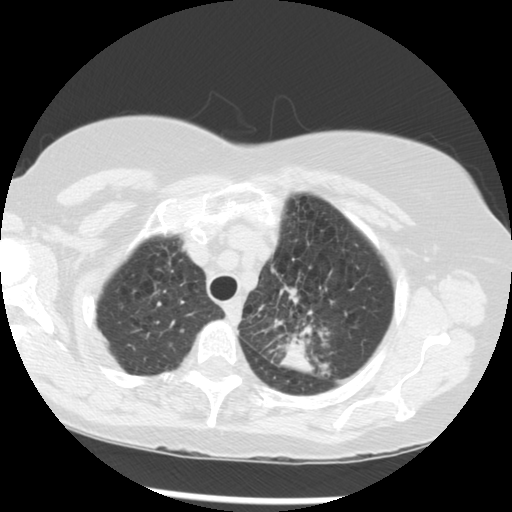
Chest CT (low-dose screening protocol), one axial image. Third screening round (two years after baseline). Lung window (W 1500 / L -600 HU). 2.5 mm slice thickness. Slice 234 of 283 in the series. 512 × 512 image matrix, field of view 330 × 330 mm. Female participant, aged 70 years at enrolment. Current smoker at enrolment.
• Expert-annotated lung lesion, bounding box (x1, y1, x2, y2) in pixels: (253, 284, 350, 372).
• Screening reader's record for this exam (one nodule recorded; not confirmed to be the boxed lesion): non-calcified nodule or mass ≥4 mm, left upper lobe, 32 × 26 mm, spiculated (stellate) margins, soft tissue attenuation, pre-existing on the prior screen: yes; interval growth: yes.
• Official screen result: positive, other.
• Lung cancer was diagnosed 24 days after this screen: neoplasm, malignant, left upper lobe, stage IIIB (AJCC 6th edition), 40 mm at pathology.